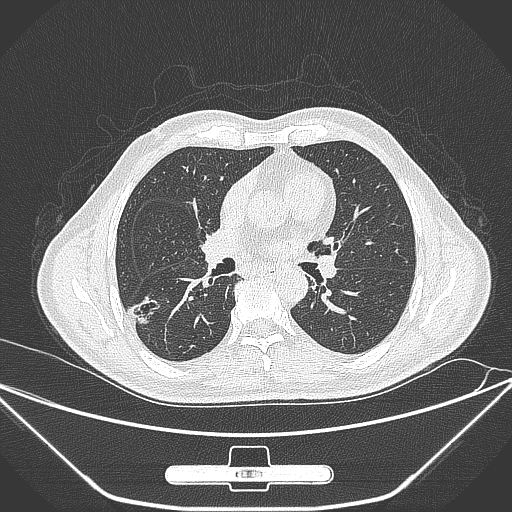
Chest CT, one axial slice. Position 151 of 309 along the scan axis. 120 kVp. Lung window (W 1500 / L -600 HU). 1 mm slice thickness. 512 × 512 image matrix, field of view 398 × 398 mm. Male patient, age 71 years. From the clinical record (not read from this slice): clinical TNM (as recorded): T1c N0 M0.
Annotated regions visible in this slice (rectangle marked by the reading radiologist):
- lung tumour (recorded histology: adenocarcinoma): bounding box [x1, y1, x2, y2] px = [127, 291, 163, 330]